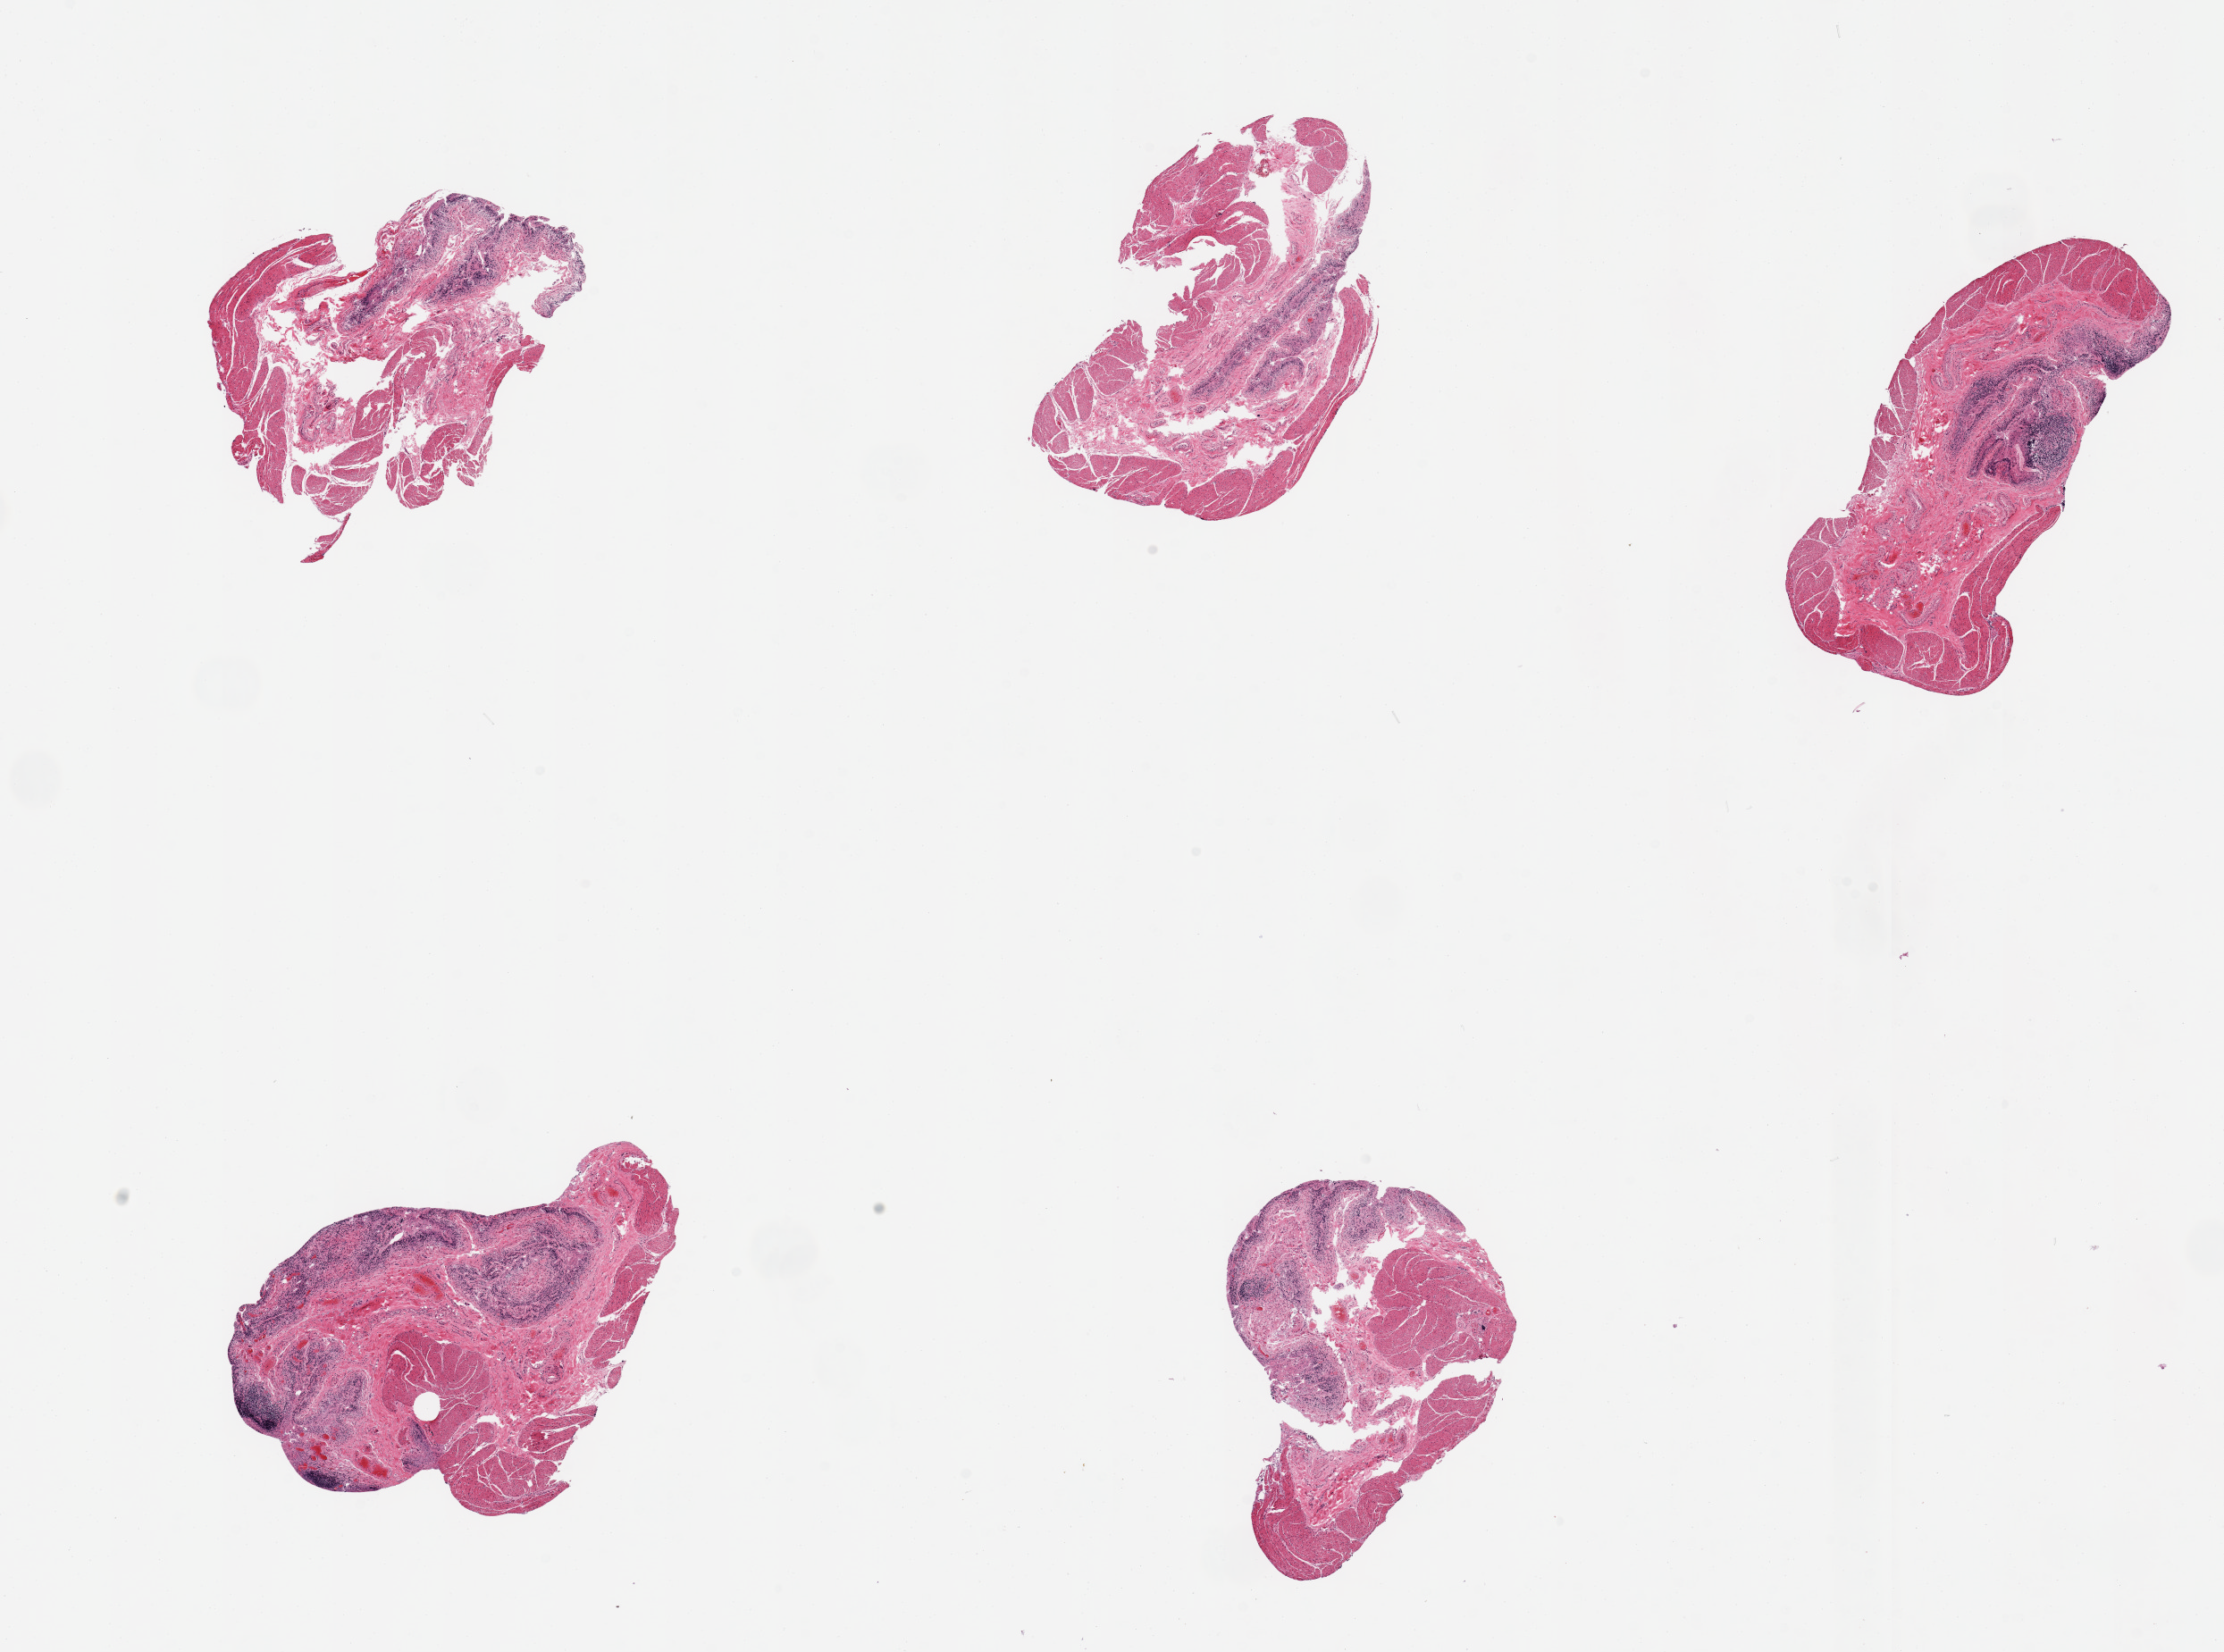
Hematoxylin and eosin (H&E) whole-slide image, a low-resolution overview of the entire scanned area, about 19.7 x 14.6 mm. PAXgene-fixed paraffin-embedded (PFPE) section. Section of ileum (target tissue). Donor tissue sample. Male donor.
Reviewer comment on this tissue sample: 5 pieces, target lymphoid aggregates are less than 1% of tissue.